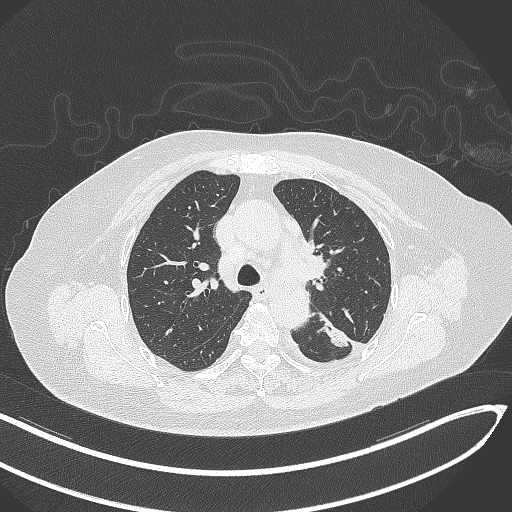
Chest CT, one axial slice. Slice 217 of 270 in the series (ordered by position). 120 kVp. Lung window (W 1500 / L -600 HU). 512 × 512 image matrix. Female patient, age 76 years. Case-level facts recorded for this patient, not image findings: clinical TNM (as recorded): T1c N0 M0.
Outlined on this slice (bounding box drawn by a radiologist):
- lung tumour (recorded histology: adenocarcinoma): bounding box <313,311,351,355> (left, top, right, bottom; pixels)